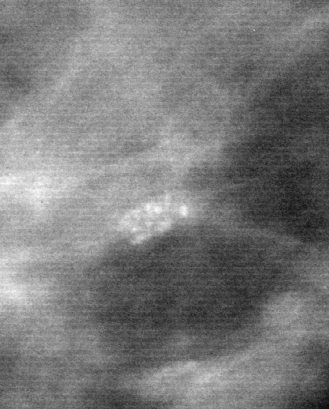
Region of interest cut from a scanned film mammogram (one marked finding); left breast; CC view; BI-RADS breast density category 2 (scale 1–4).
- Calcifications, morphology pleomorphic, distribution clustered; BI-RADS assessment category 4; subtlety rating 4 on a 1 (subtle) to 5 (obvious) scale; pathology (as recorded): benign.